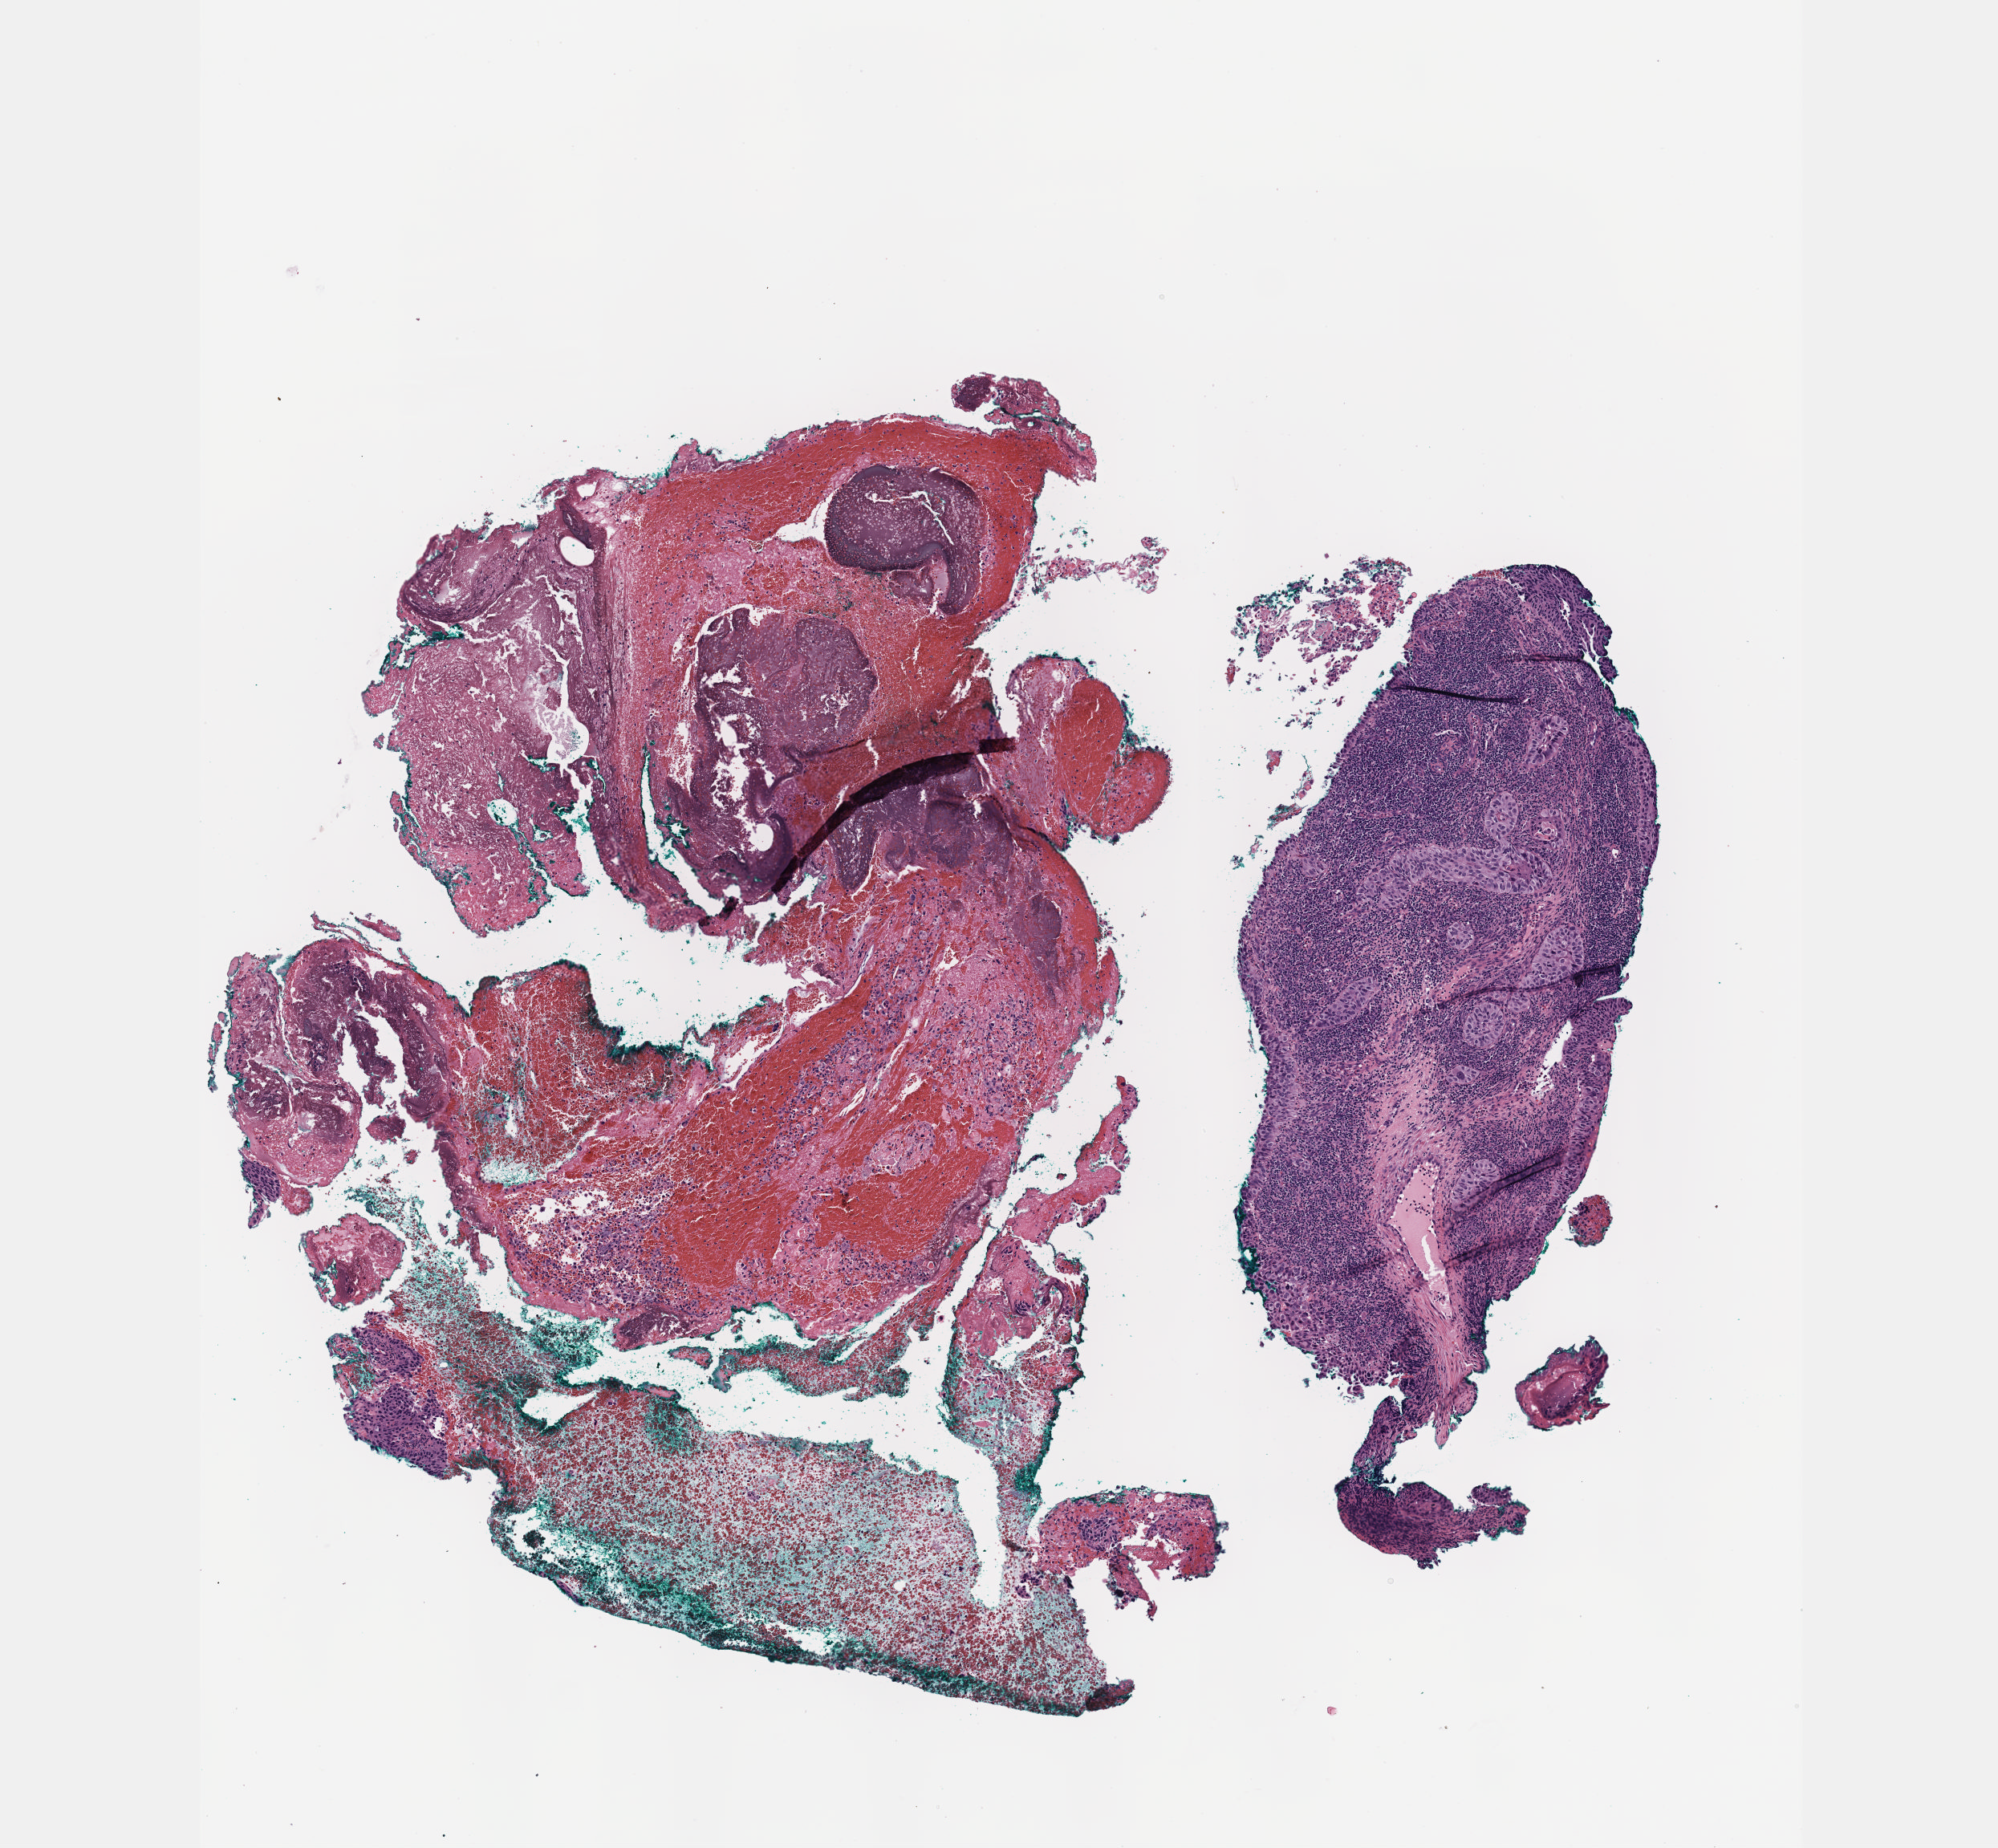
Digitized H&E tissue section (whole slide) — a low-resolution overview of the entire scanned area, about 5.0 x 4.7 mm (acquisition: 40x scan). Formalin-fixed paraffin-embedded (FFPE) diagnostic section. Cervix, primary tumour sample. Female patient; age at initial diagnosis 38 years. Histologic grade: GX (grade cannot be assessed).
Diagnosis: Squamous cell carcinoma, NOS (cervix uteri). FIGO stage: IIB.